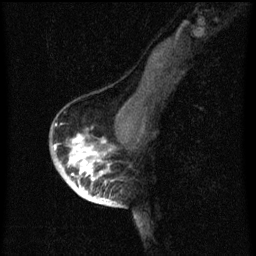
Breast MRI (dynamic contrast-enhanced), one sagittal slice; position 41 of 60 along the scan axis; dynamic contrast-enhanced series, image 2 of 3 at this slice position (ordered by acquisition); 1.5 T; TE 4.2 ms, TR 8 ms; 2 mm slice thickness; 256 × 256 image matrix. Patient: female, 56 years.
Annotated regions visible in this slice (semi-automatic segmentation, software-assisted and operator-edited):
- analysis volume of interest (the breast-tissue region the enhancement analysis was run in; not a lesion): bounding box (x1, y1, x2, y2) in pixels: (54, 122, 120, 199)
- tumour enhancement mask (voxels above the 70 % enhancement threshold inside the analysis volume of interest): (54, 124, 113, 199)